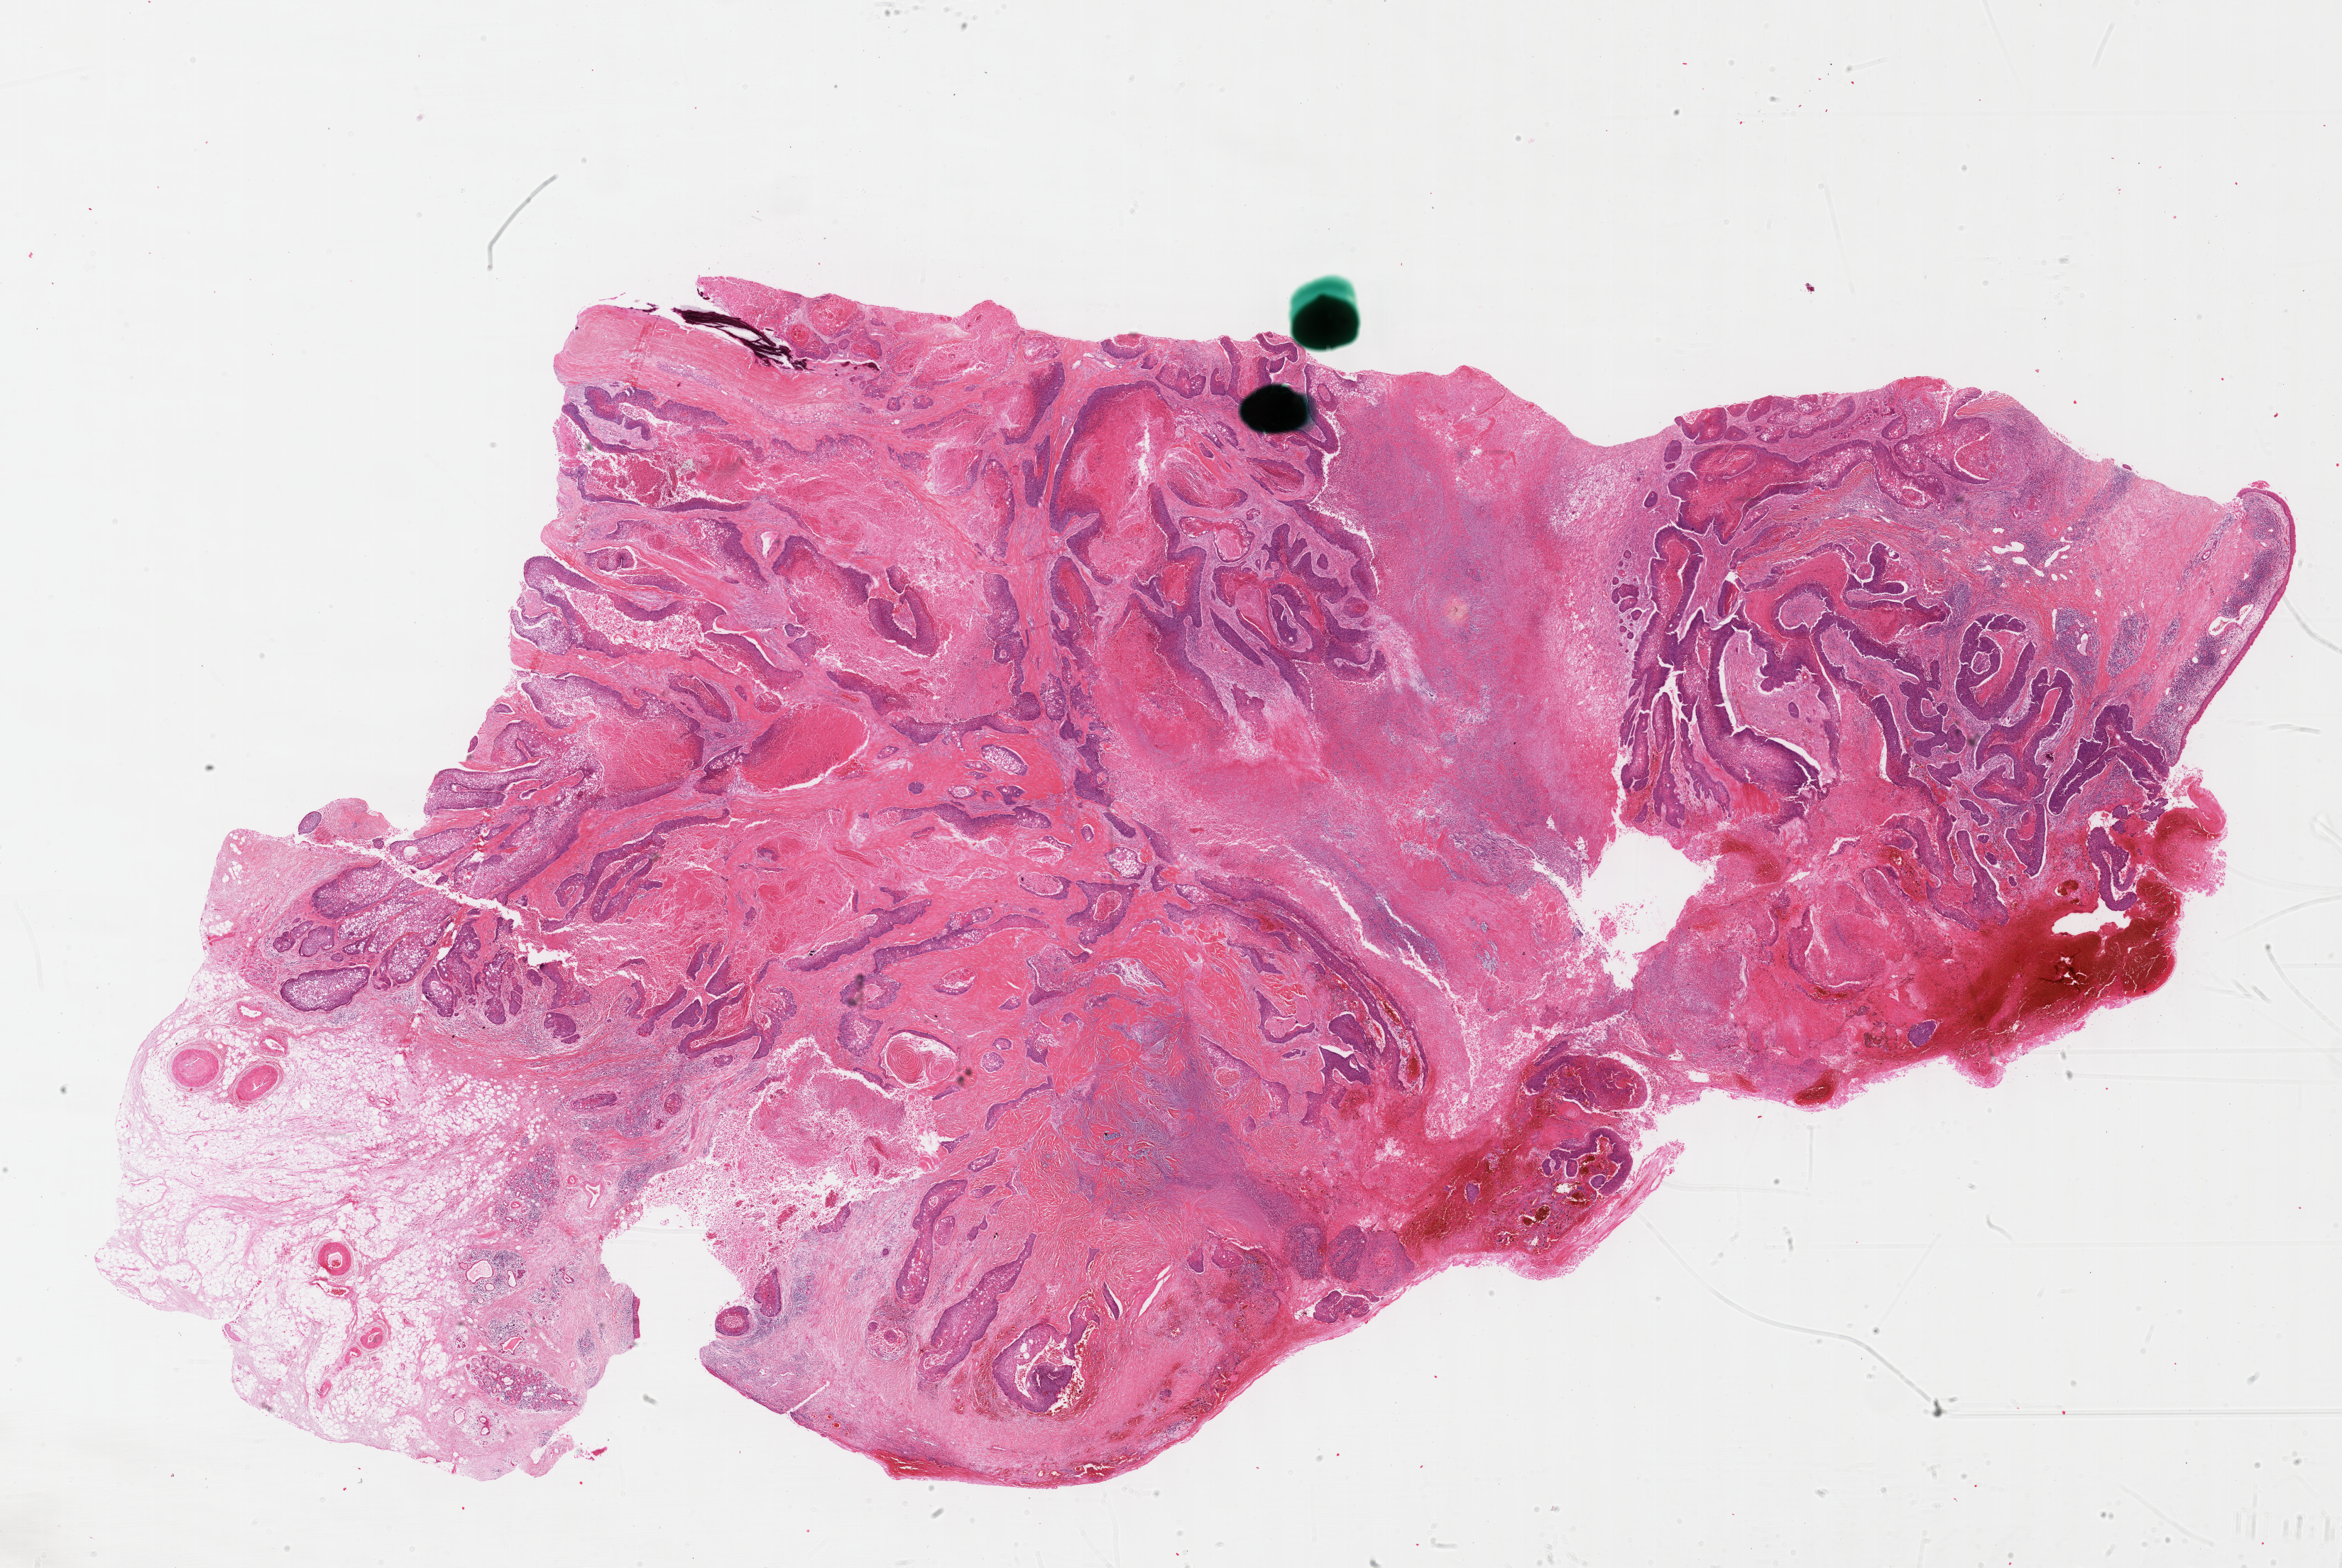
Whole-slide histology image, Hematoxylin and eosin (H&E) stained — low-resolution overview of the scanned area, about 26.7 x 17.9 mm (acquisition: 40x scan). FFPE section. Sample: primary tumour, head and neck. Male, age 80 years at initial diagnosis. Histologic grade: G2 (moderately differentiated).
TNM: T2 NX. AJCC pathologic stage: II (7th edition). Histologic diagnosis: Squamous cell carcinoma, NOS (larynx, NOS).